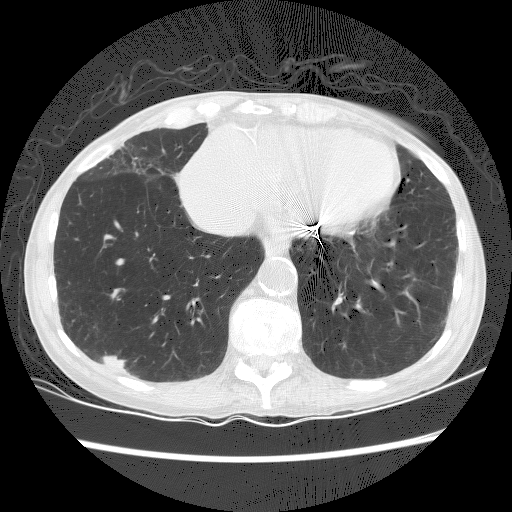
Low-dose screening chest CT, axial slice. First (baseline) screen. Lung window (W 1500 / L -600 HU). 2.5 mm slice thickness. Female participant, aged 70 years at enrolment. Current smoker at enrolment.
Expert reader's lesion annotation, bounding box <93,344,145,384> (left, top, right, bottom; pixels). The screening reader recorded 2 non-calcified nodules or masses ≥4 mm on this exam (right lower lobe, left lower lobe); which of them this box marks is not recorded. Later outcome: lung cancer diagnosed 125 days after this screen — squamous cell carcinoma, NOS, right lower lobe, well differentiated (G1), stage IA (AJCC 6th edition), 25 mm at pathology.